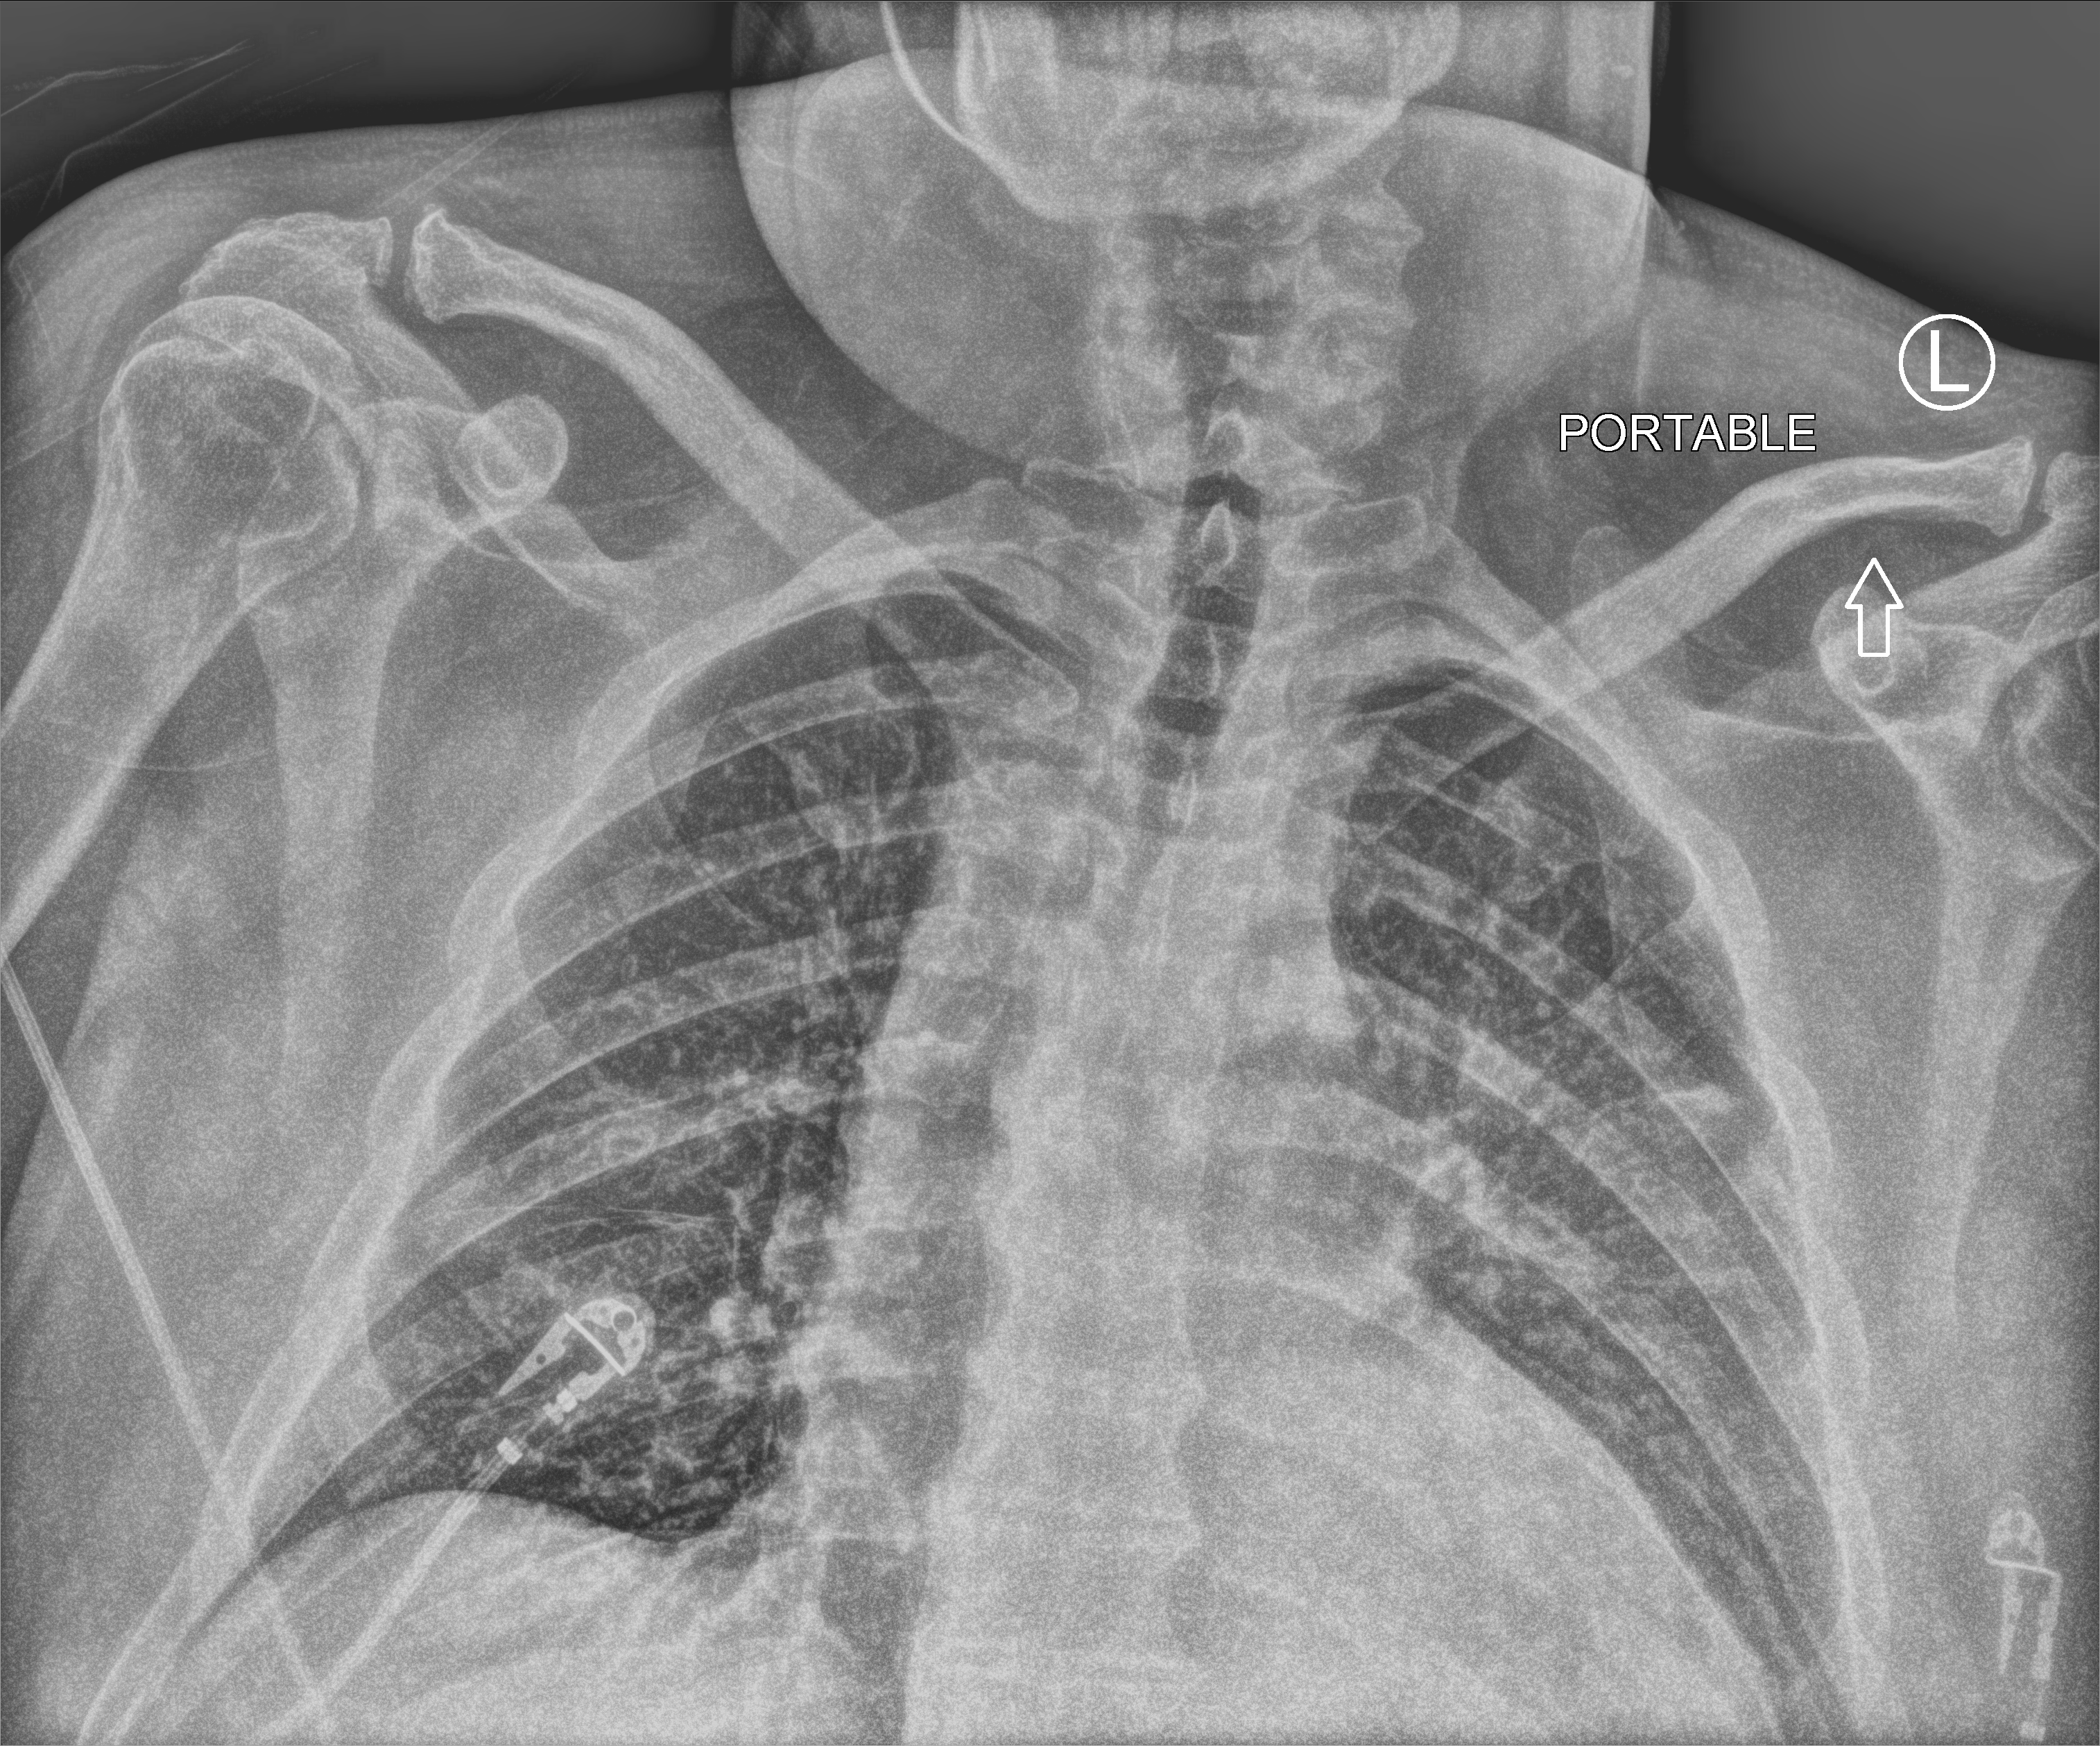
Chest X-ray (portable), anteroposterior (AP) projection. Patient hospitalised with COVID-19; male, aged 18–59 years.
Hospital-stay facts (about this admission, not read from this image; timing relative to this image not recorded):
- mechanically ventilated during this hospital stay: no